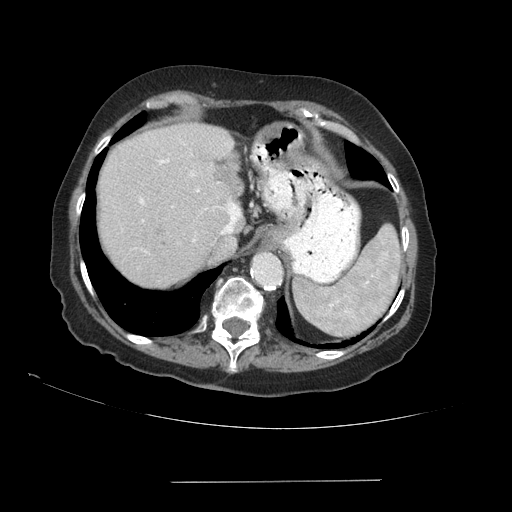
Contrast-enhanced abdominal CT (liver protocol), one axial slice. Position 71 of 89 along the scan axis. Reconstruction kernel STANDARD. Soft-tissue window (W 400 / L 40 HU). 512 × 512 image matrix. From the clinical record (not read from this slice): diagnosis: hepatocellular carcinoma (patient treated with transarterial chemoembolisation; whether this scan precedes or follows treatment is not stated here); TNM stage (as recorded): Stage-IVA.
Outlined on this slice (semi-automatic segmentation, software-assisted and operator-edited):
- abdominal aorta: bounding box [x1, y1, x2, y2] px = [253, 255, 279, 284]
- liver parenchyma outside the tumour (the mass and vessels are separate outlines, so this box may not span the whole liver): [98, 122, 242, 288]
- liver vessels: [139, 159, 241, 252]